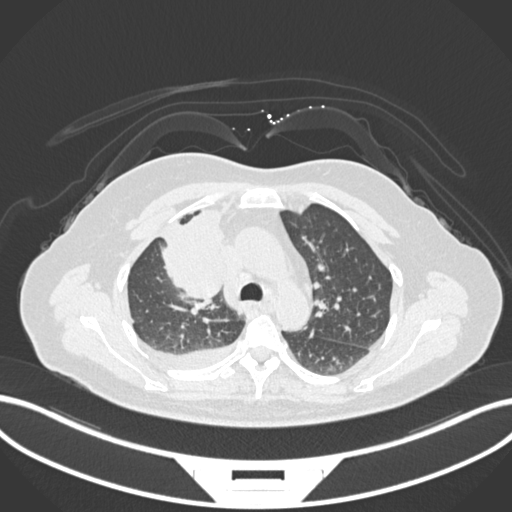
Chest CT, one axial slice. Slice 108 of 172 in the series (ordered by position). Reconstruction kernel B30f. 120 kVp. Lung window (W 1500 / L -600 HU). 1 mm slice thickness. 512 × 512 image matrix, field of view 400 × 400 mm. Female patient, age 52 years. Case-level facts recorded for this patient, not image findings: clinical TNM (as recorded): T3 N1 M1.
Annotated regions visible in this slice (bounding box drawn by a radiologist):
- lung tumour (recorded histology: adenocarcinoma): bounding box [x1, y1, x2, y2] px = [159, 208, 226, 304]